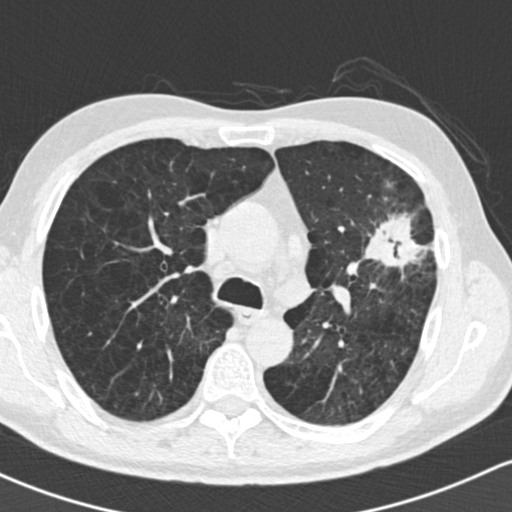
Low-dose screening chest CT, one axial slice. Position 103 of 162 along the scan axis. Reconstruction kernel B30f. Lung window (W 1500 / L -600 HU). 2 mm slice thickness. 512 × 512 image matrix.
Structures marked on this image (outlined manually by an expert reader):
- lesion 1 (tumor, upper lobe of left lung): box from (x=364, y=212) to (x=425, y=275) px